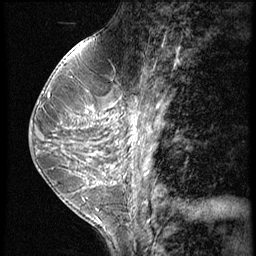
Breast MRI (dynamic contrast-enhanced), one sagittal slice; slice 27 of 60 in the series (ordered by position); 3 images stored at this slice position (order not interpretable as contrast timing); 1.5 T; TE 4.2 ms, TR 9 ms; 2.5 mm slice thickness; 256 × 256 image matrix, field of view 180 × 180 mm. Female patient, age 38 years. Case-level facts recorded for this patient, not image findings: setting: breast cancer imaged before/during neoadjuvant chemotherapy; receptor status: triple-negative.
Annotated regions visible in this slice (semi-automatic segmentation, software-assisted and operator-edited):
- analysis volume of interest (the breast-tissue region the enhancement analysis was run in; not a lesion): bounding box [x1, y1, x2, y2] px = [119, 93, 165, 150]
- tumour enhancement mask (voxels above the 140 % enhancement threshold inside the analysis volume of interest): [158, 104, 165, 109]